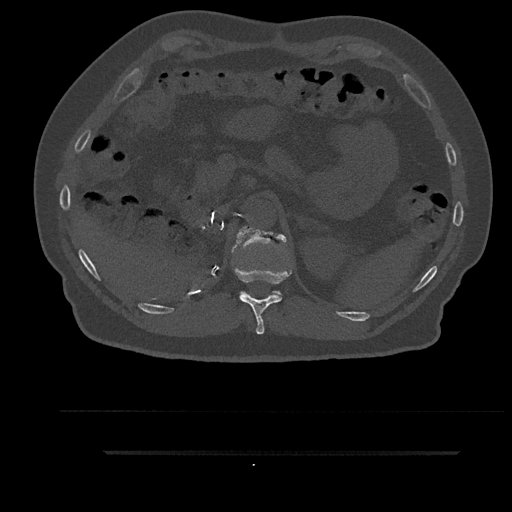
CT including the spine, one axial slice. Position 282 of 797 along the scan axis. Reconstruction kernel Br40s/3. 120 kVp. Bone window (W 1800 / L 400 HU). 0.5 mm slice thickness. 512 × 512 image matrix. Male patient, age 63 years. Case-level facts recorded for this patient, not image findings: primary cancer: renal; vertebrae with lytic lesions (as recorded): T8.
Outlined on this slice (semi-automatically segmented with operator editing):
- T11 vertebra: bounding box [x1, y1, x2, y2] px = [235, 232, 291, 335]
- T12 vertebra: [231, 226, 286, 295]